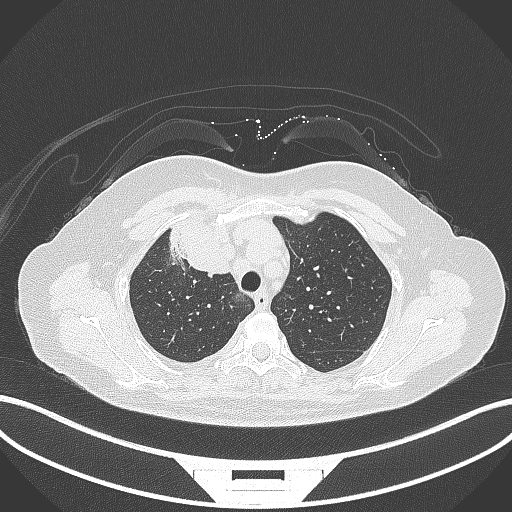
Chest CT, one axial slice. Slice 236 of 305 in the series (ordered by position). 120 kVp. Lung window (W 1500 / L -600 HU). 1 mm slice thickness. 512 × 512 image matrix. Patient: female, 52 years. Case-level facts recorded for this patient, not image findings: clinical TNM (as recorded): T3 N1 M1.
Outlined on this slice (rectangle marked by the reading radiologist):
- lung tumour (recorded histology: adenocarcinoma): box from (x=169, y=215) to (x=233, y=278) px